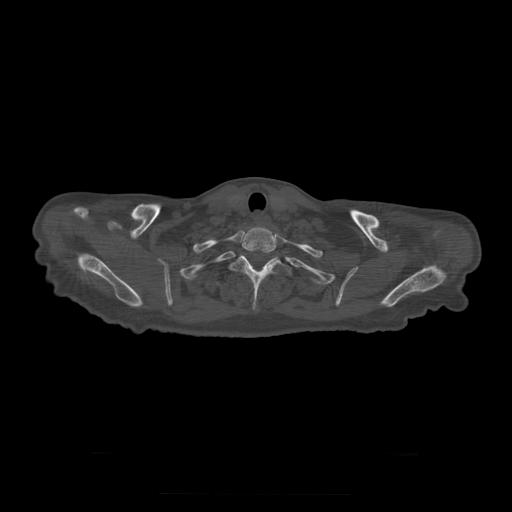
CT including the spine, one axial slice. Slice 279 of 397 in the series (ordered by position). Bone window (W 1800 / L 400 HU). 1.25 mm slice thickness. 512 × 512 image matrix, field of view 510 × 510 mm. Patient age 73 years. From the clinical record (not read from this slice): primary cancer: prostate.
Structures marked on this image (semi-automatic segmentation, software-assisted and operator-edited):
- T1 vertebra: bounding box <238,231,276,253> (left, top, right, bottom; pixels)
- T2 vertebra: <230,255,292,310>
- T3 vertebra: <225,283,229,288>